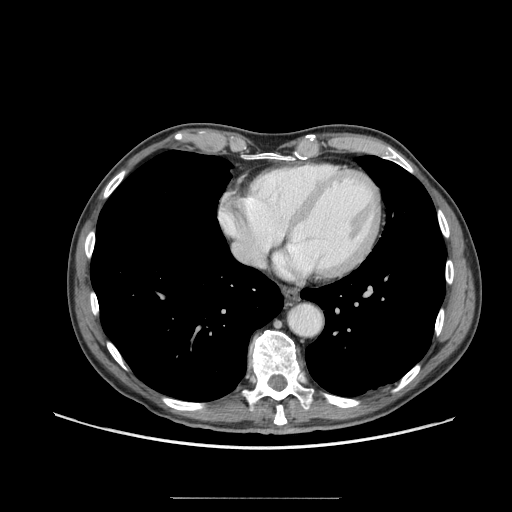
Contrast-enhanced abdominal CT (liver protocol), one axial slice. Slice 71 of 71 in the series (ordered by position). 140 kVp. Soft-tissue window (W 400 / L 40 HU). 512 × 512 image matrix, field of view 400 × 400 mm. Case-level facts recorded for this patient, not image findings: diagnosis: hepatocellular carcinoma (patient treated with transarterial chemoembolisation; whether this scan precedes or follows treatment is not stated here); TNM stage (as recorded): Stage-I; Child-Pugh class: A; tumour differentiation: well differentiated.
Structures marked on this image (semi-automatic segmentation, software-assisted and operator-edited):
- abdominal aorta: bounding box [x1, y1, x2, y2] px = [289, 304, 321, 336]